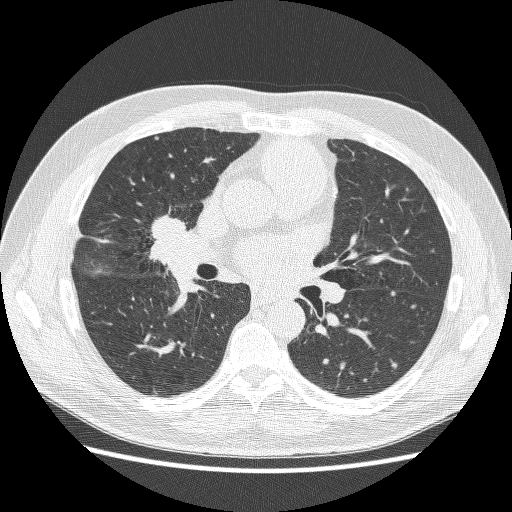
Axial slice from a low-dose chest CT screening exam. First (baseline) screen. Lung window (W 1500 / L -600 HU). Lung (sharp) reconstruction kernel (BONE). 120 kVp. 512 × 512 image matrix. Male, age 59 years at enrolment. Former smoker at enrolment.
Lesion marked by an expert reader, bounding box (x1, y1, x2, y2) in pixels: (129, 208, 198, 272). Screening reader's record for this exam: no non-calcified nodule ≥4 mm recorded. Later outcome: lung cancer diagnosed 24 days after this screen — adenocarcinoma, NOS, right middle lobe, poorly differentiated (G3), stage IV (AJCC 6th edition), 54 mm at pathology.